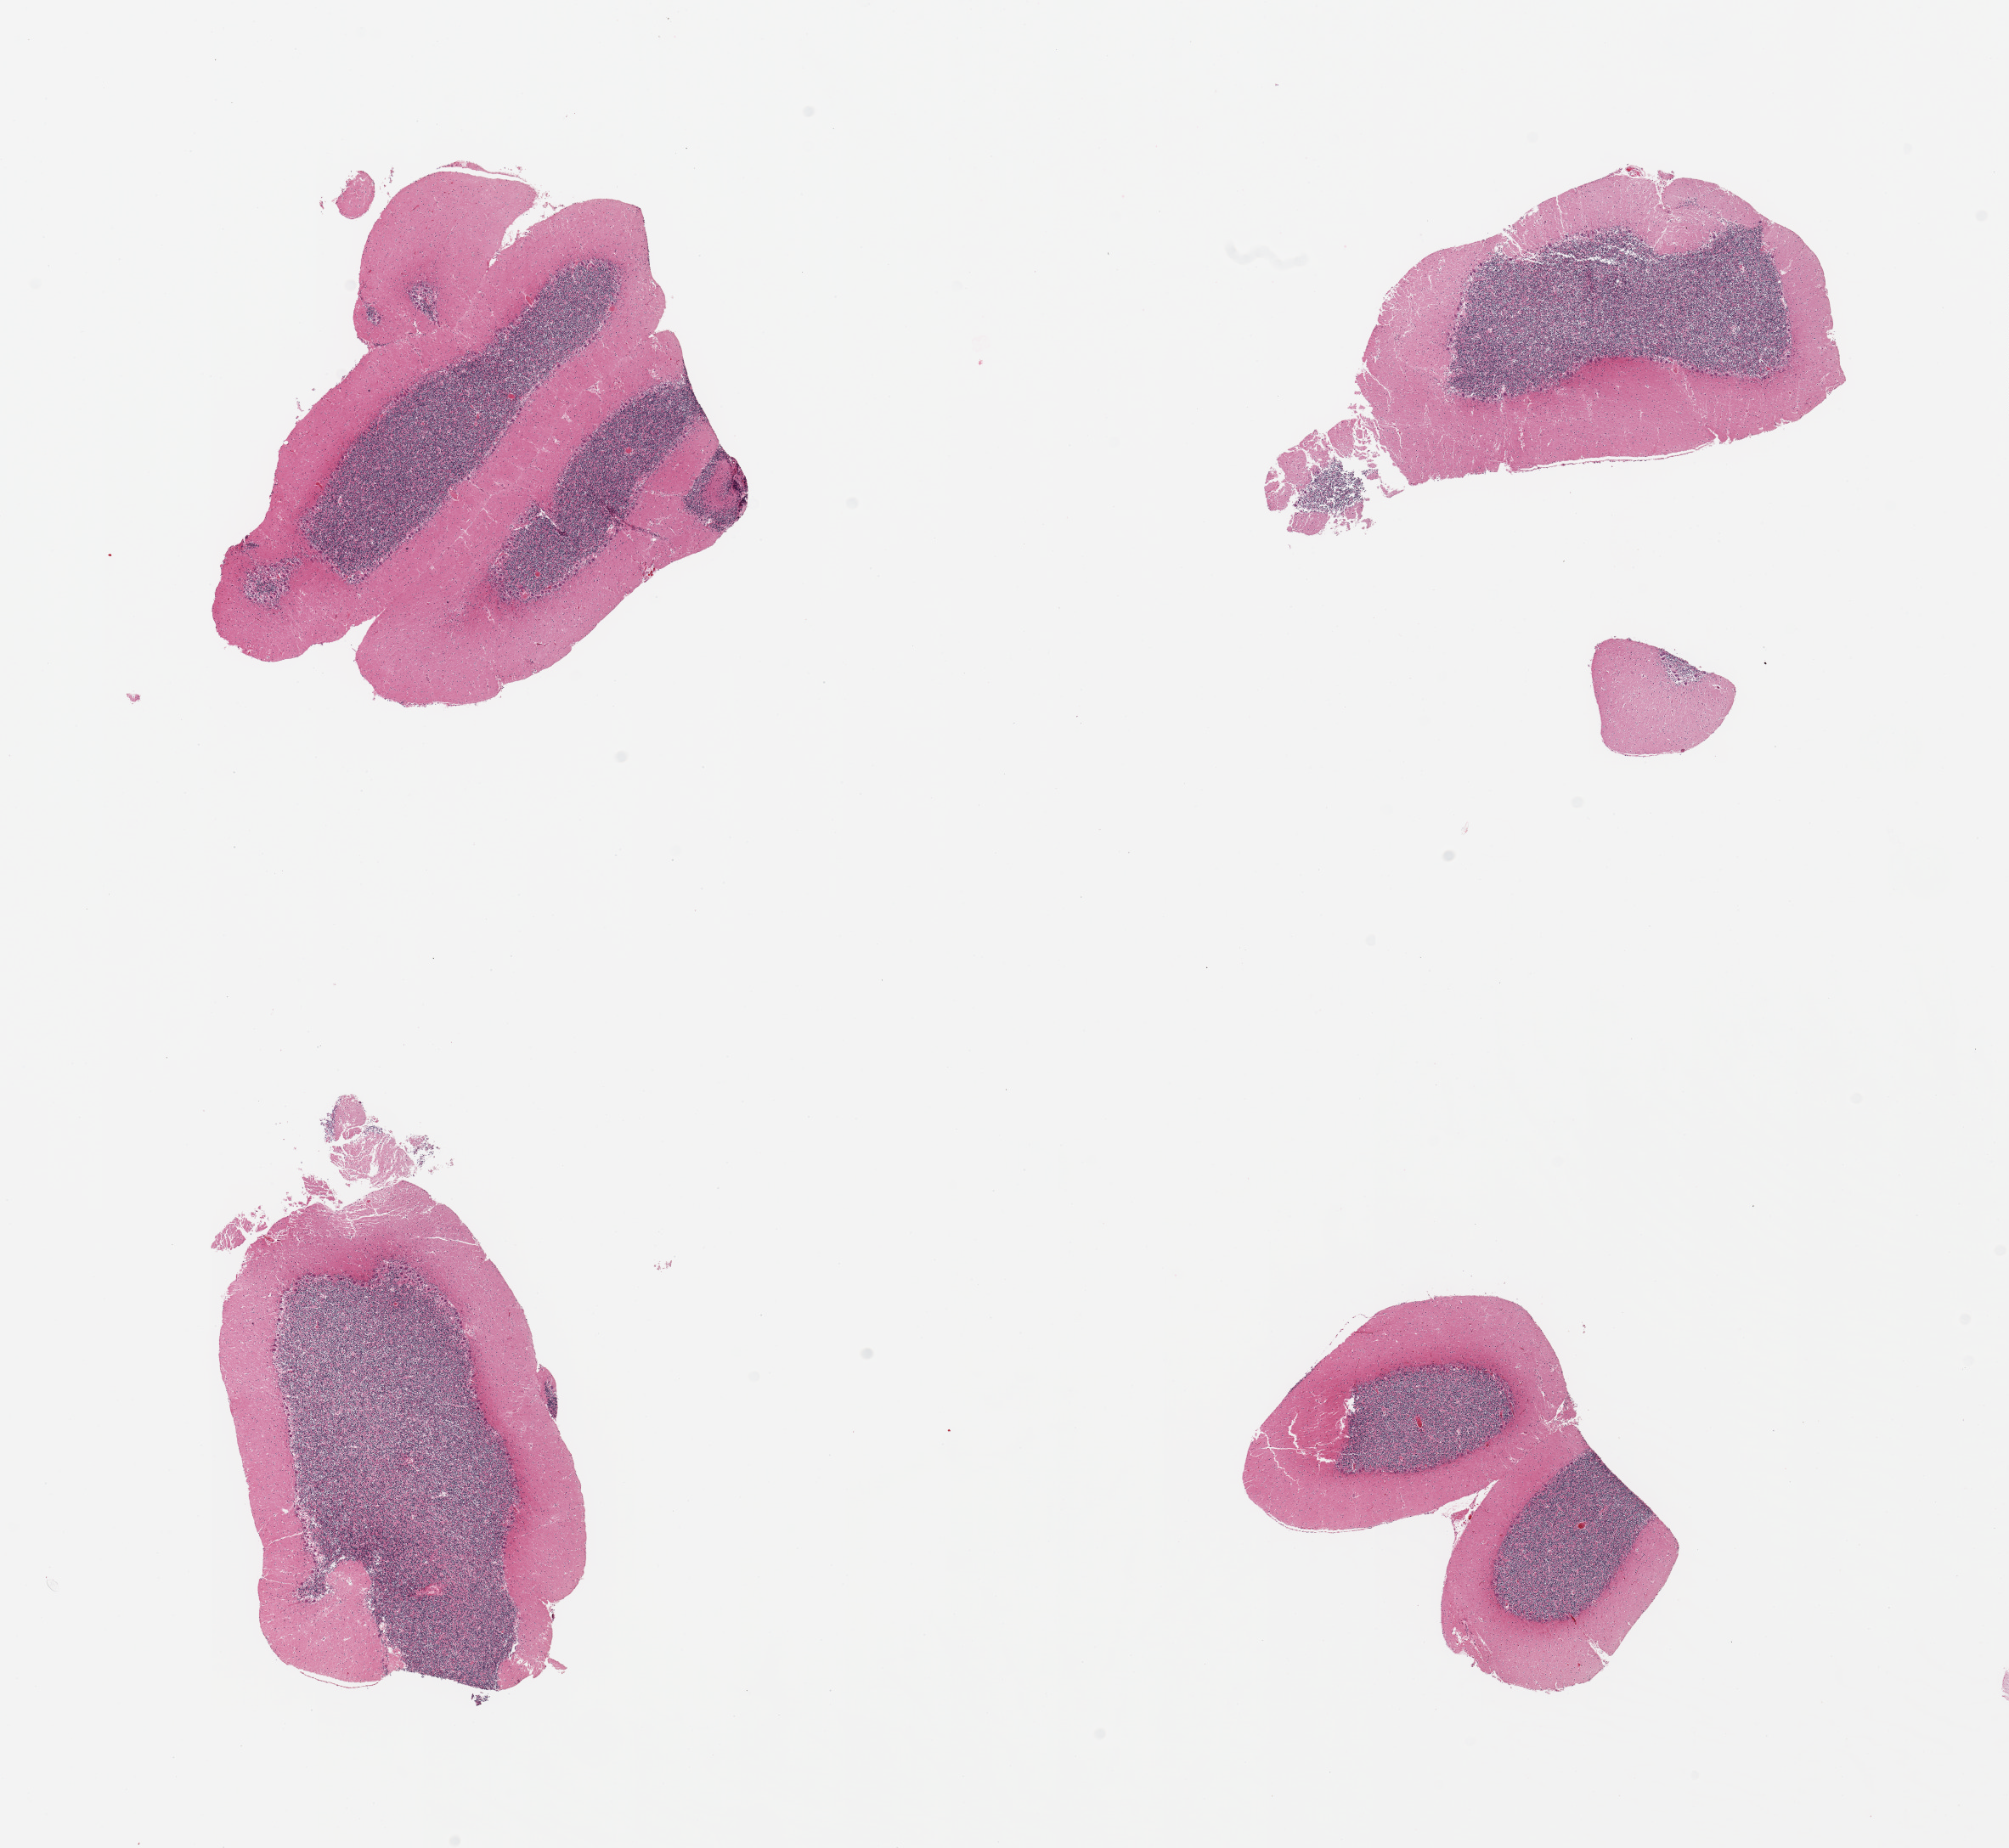
Digitized hematoxylin and eosin (H&E)-stained section — low-resolution overview of the scanned area, about 18.7 x 17.2 mm; PAXgene-fixed paraffin-embedded (PFPE) section; target tissue: cerebellum; donor tissue sample.
Pathologist's review note for this sample: 4 pieces; Purkinje cells well visualized, no evidence of hypoxic damage.